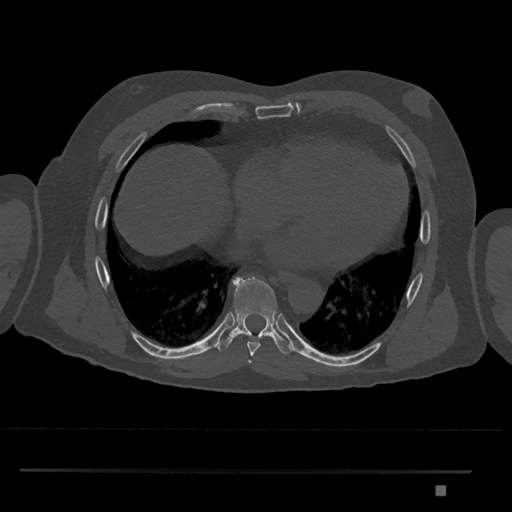
CT including the spine, one axial slice. Slice 1131 of 1134 in the series (ordered by position). Reconstruction kernel Br40s/3. 120 kVp. Bone window (W 1800 / L 400 HU). 0.5 mm slice thickness. 512 × 512 image matrix, field of view 429 × 429 mm. Male patient, age 65 years. From the clinical record (not read from this slice): primary cancer: prostate.
Structures marked on this image (semi-automatically segmented with operator editing):
- T8 vertebra: box from (x=216, y=277) to (x=293, y=356) px